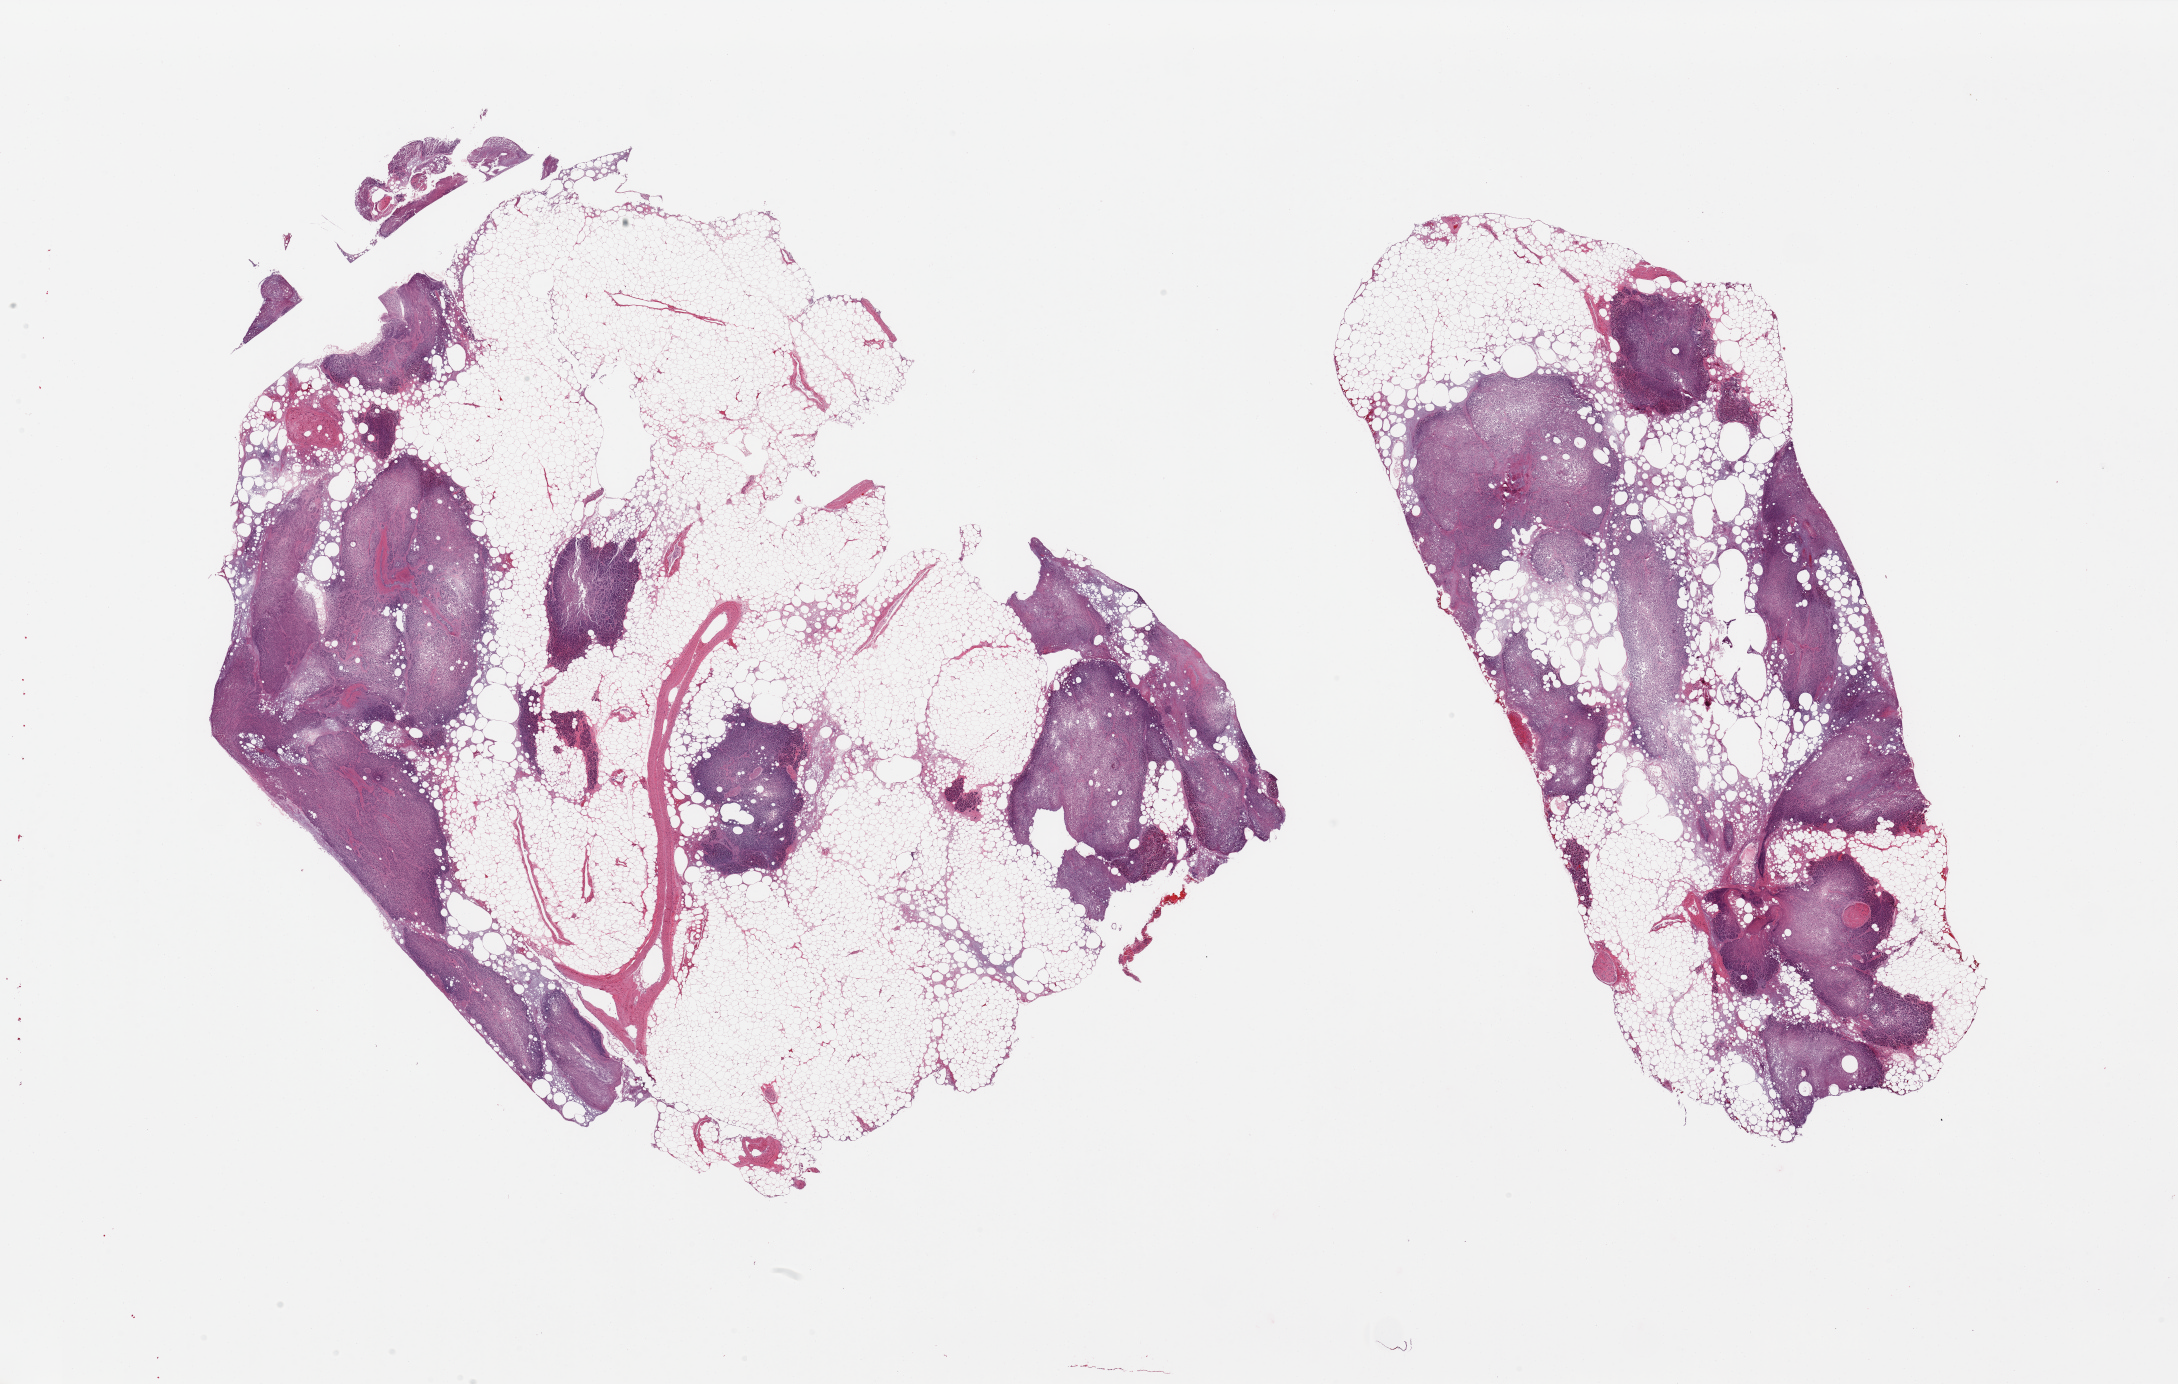
Digitized hematoxylin and eosin (H&E)-stained section, brightfield, whole scanned area (about 34.5 x 21.9 mm, acquisition: 20x scan) shown as a low-resolution overview; PAXgene-fixed, paraffin-embedded tissue; target tissue: pancreas; donor tissue sample. Donor: male.
Pathologist's review note for this sample: 2 pieces, only ~40% parenchyma; rest is fat, but badly autolyzed/saponified. Islets not visualized.